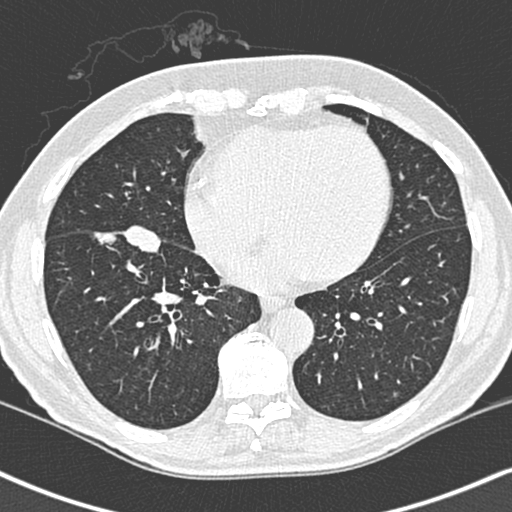
Low-dose screening chest CT, one axial slice; position 105 of 248 along the scan axis; 120 kVp; lung window (W 1500 / L -600 HU); 1.3 mm slice thickness; 512 × 512 image matrix, field of view 323 × 323 mm.
Structures marked on this image (expert manual segmentation):
- lesion 1 (tumor, lower lobe of right lung): bounding box <94,187,162,217> (left, top, right, bottom; pixels)